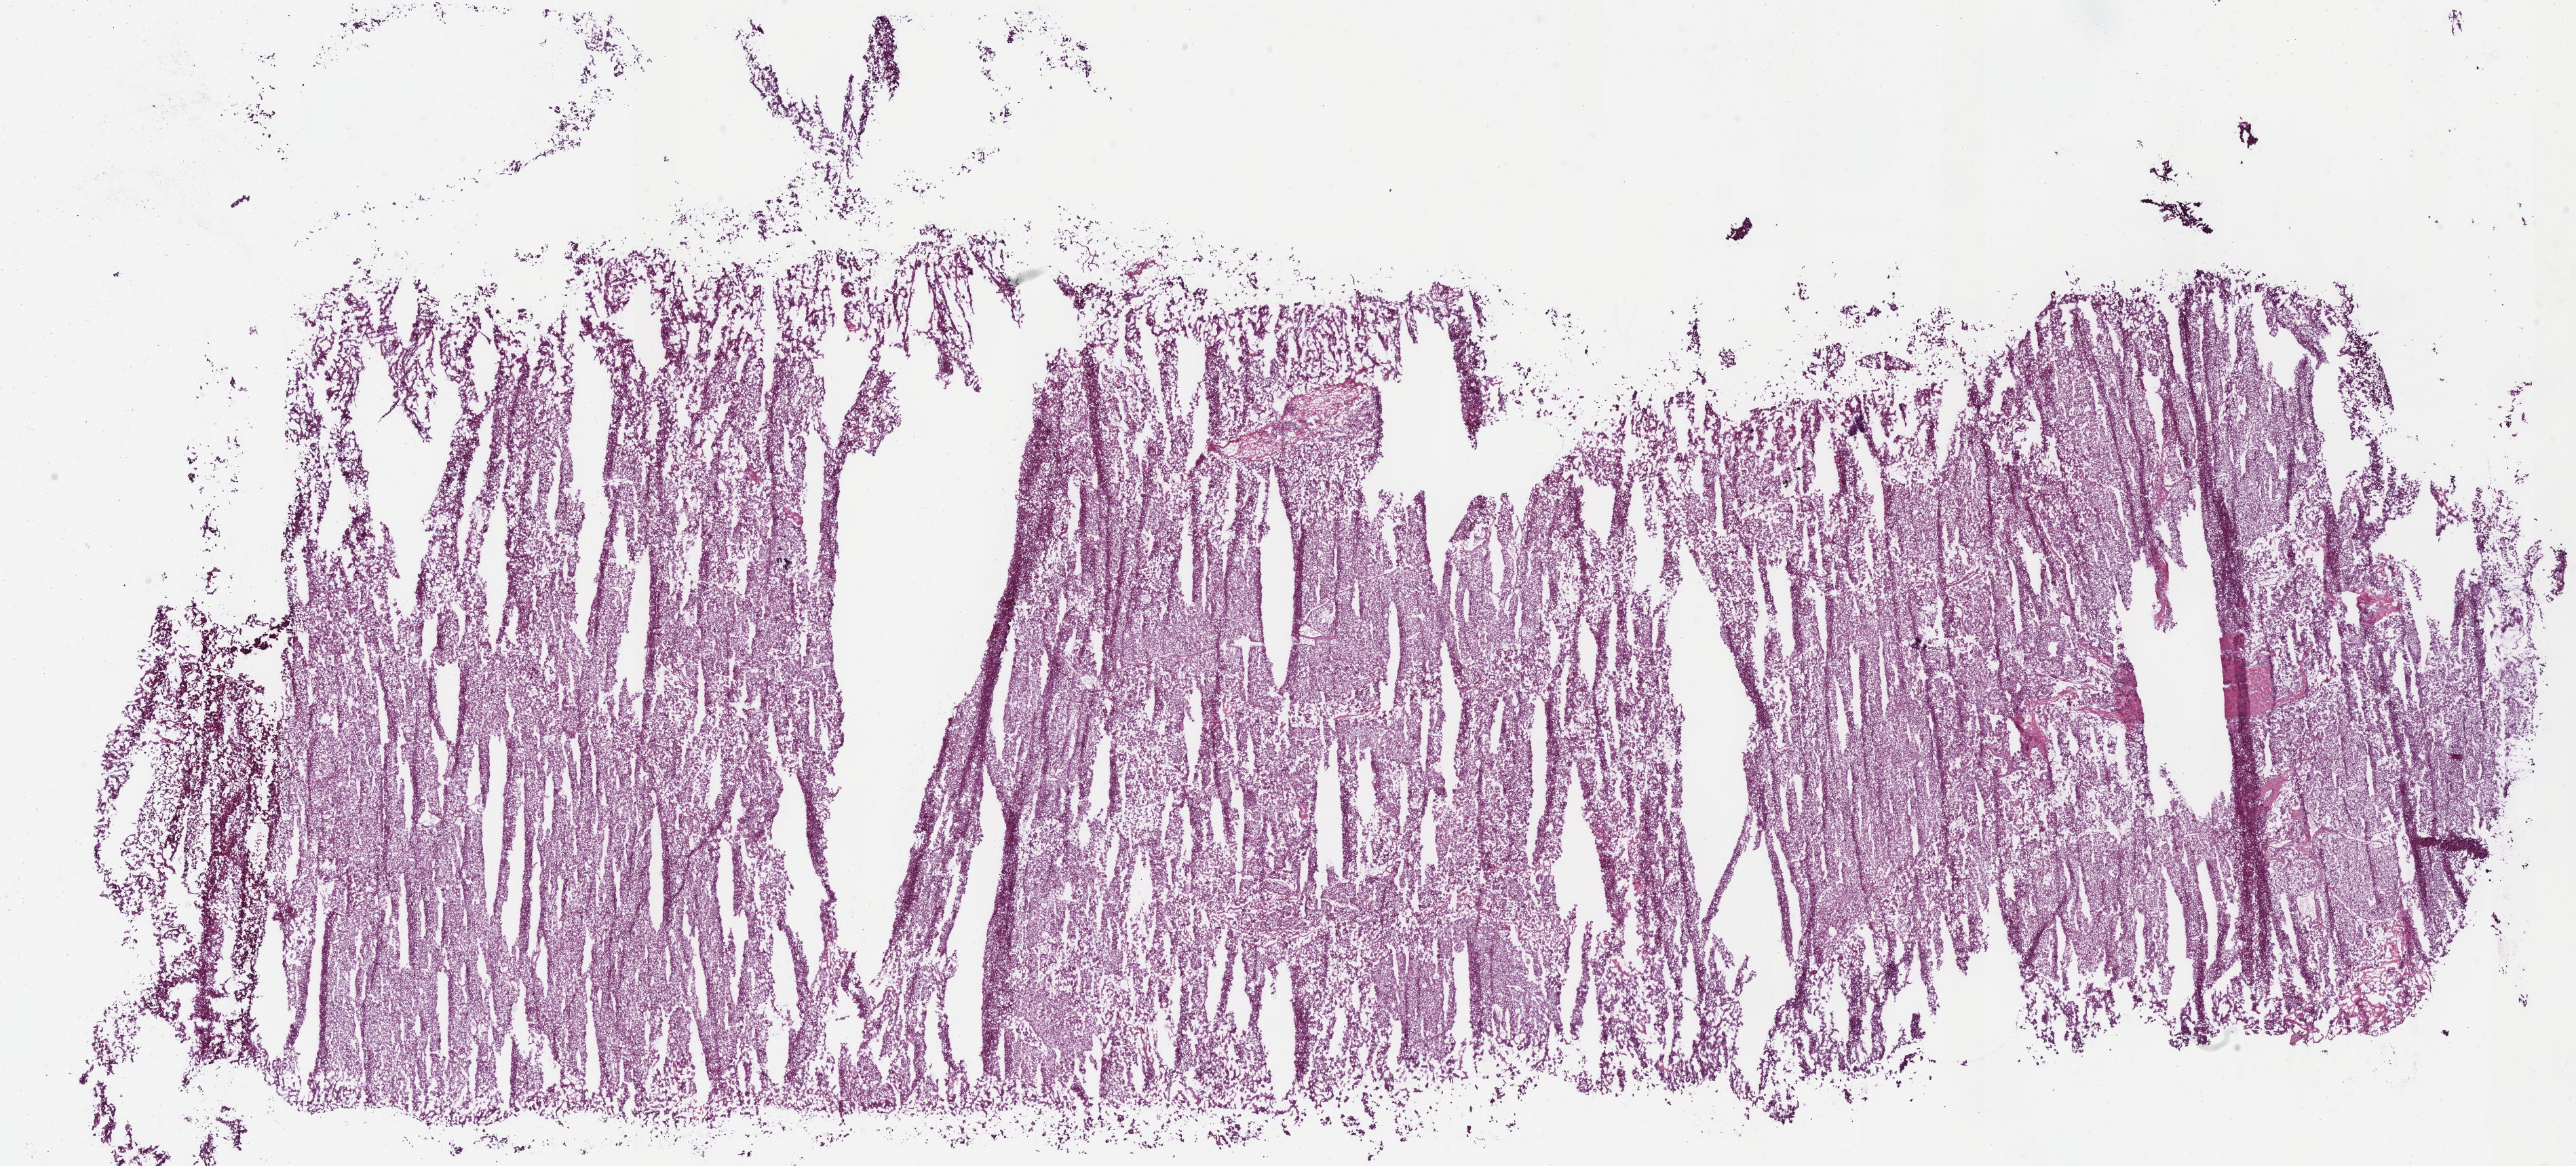
Hematoxylin and eosin (H&E) stained whole-slide image — a low-resolution overview of the entire scanned area, about 29.9 x 13.5 mm (slide scanned at 40x). Frozen section. Primary tumour sample from the kidney. Male patient; age at initial diagnosis 47 years. Slide review estimates, as recorded: tumour cells 90%, tumour nuclei 90%, normal cells 0%, stromal cells 10%, necrosis 0%.
AJCC pathologic stage: III (7th edition). Lymph nodes positive (case pathology): 3 of 3 examined. Diagnosis: Renal cell carcinoma, chromophobe type. Laterality: left.